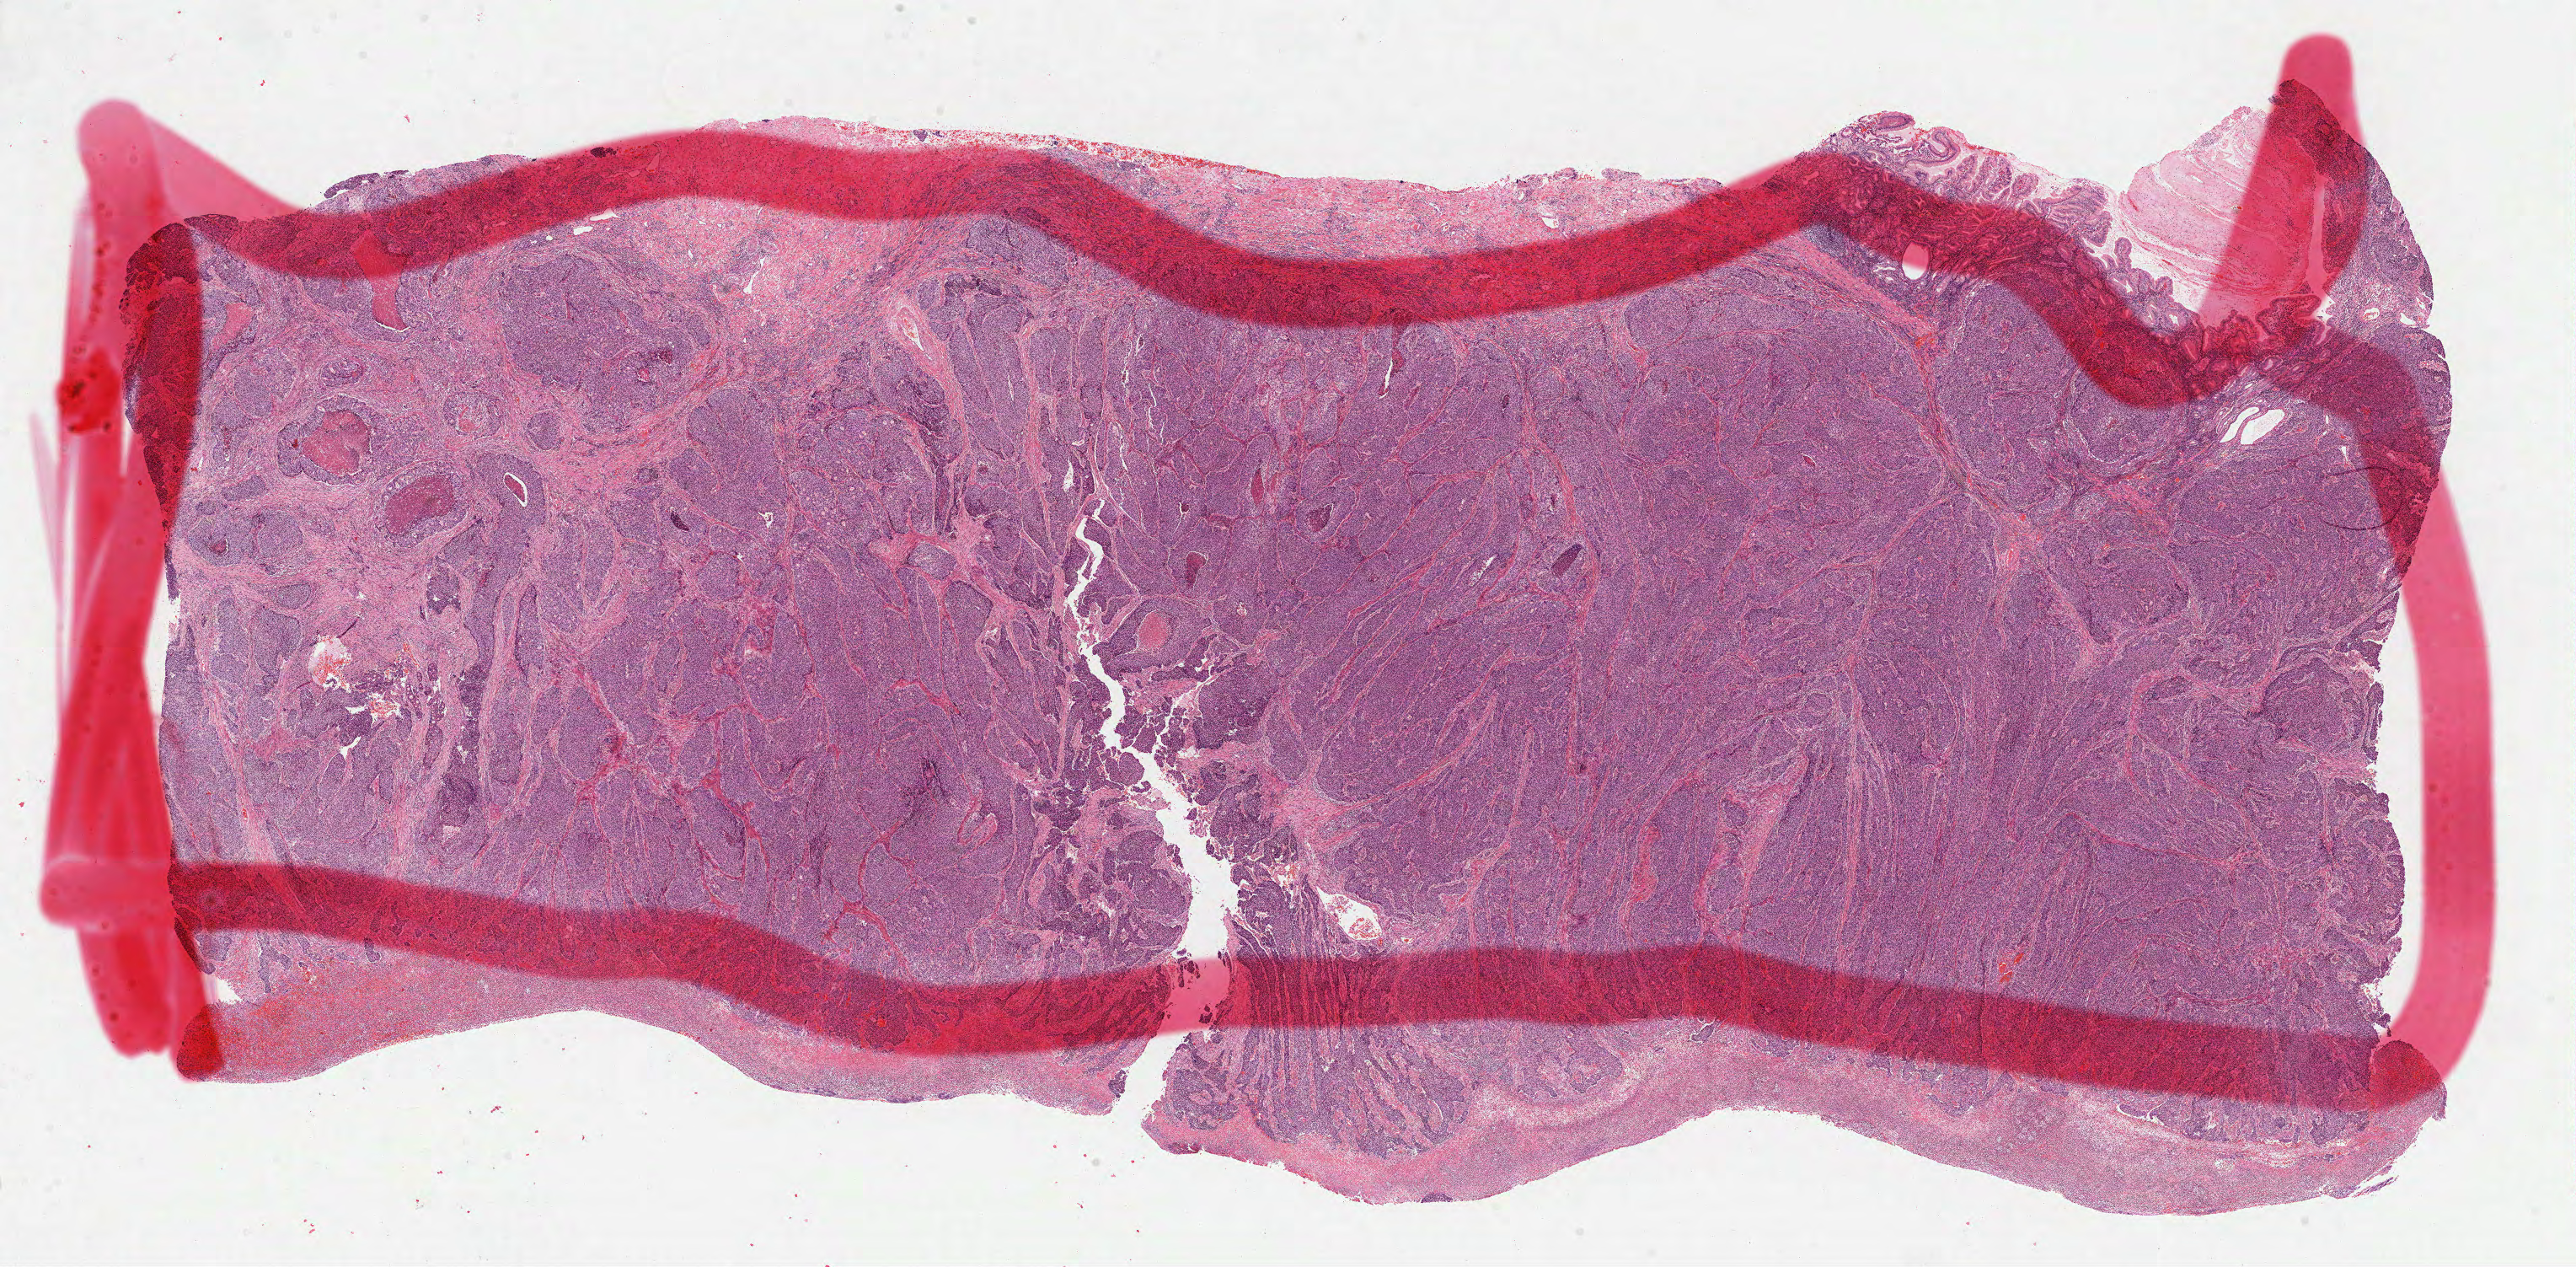
Whole-slide histology image, H&E, shown as a low-resolution overview of the whole scanned area (about 24.7 x 12.1 mm, slide scanned at 40x); formalin-fixed paraffin-embedded (FFPE) diagnostic section; sample: primary tumour, stomach. Female, age 69 years at initial diagnosis.
Histologic diagnosis: Adenocarcinoma, intestinal type.